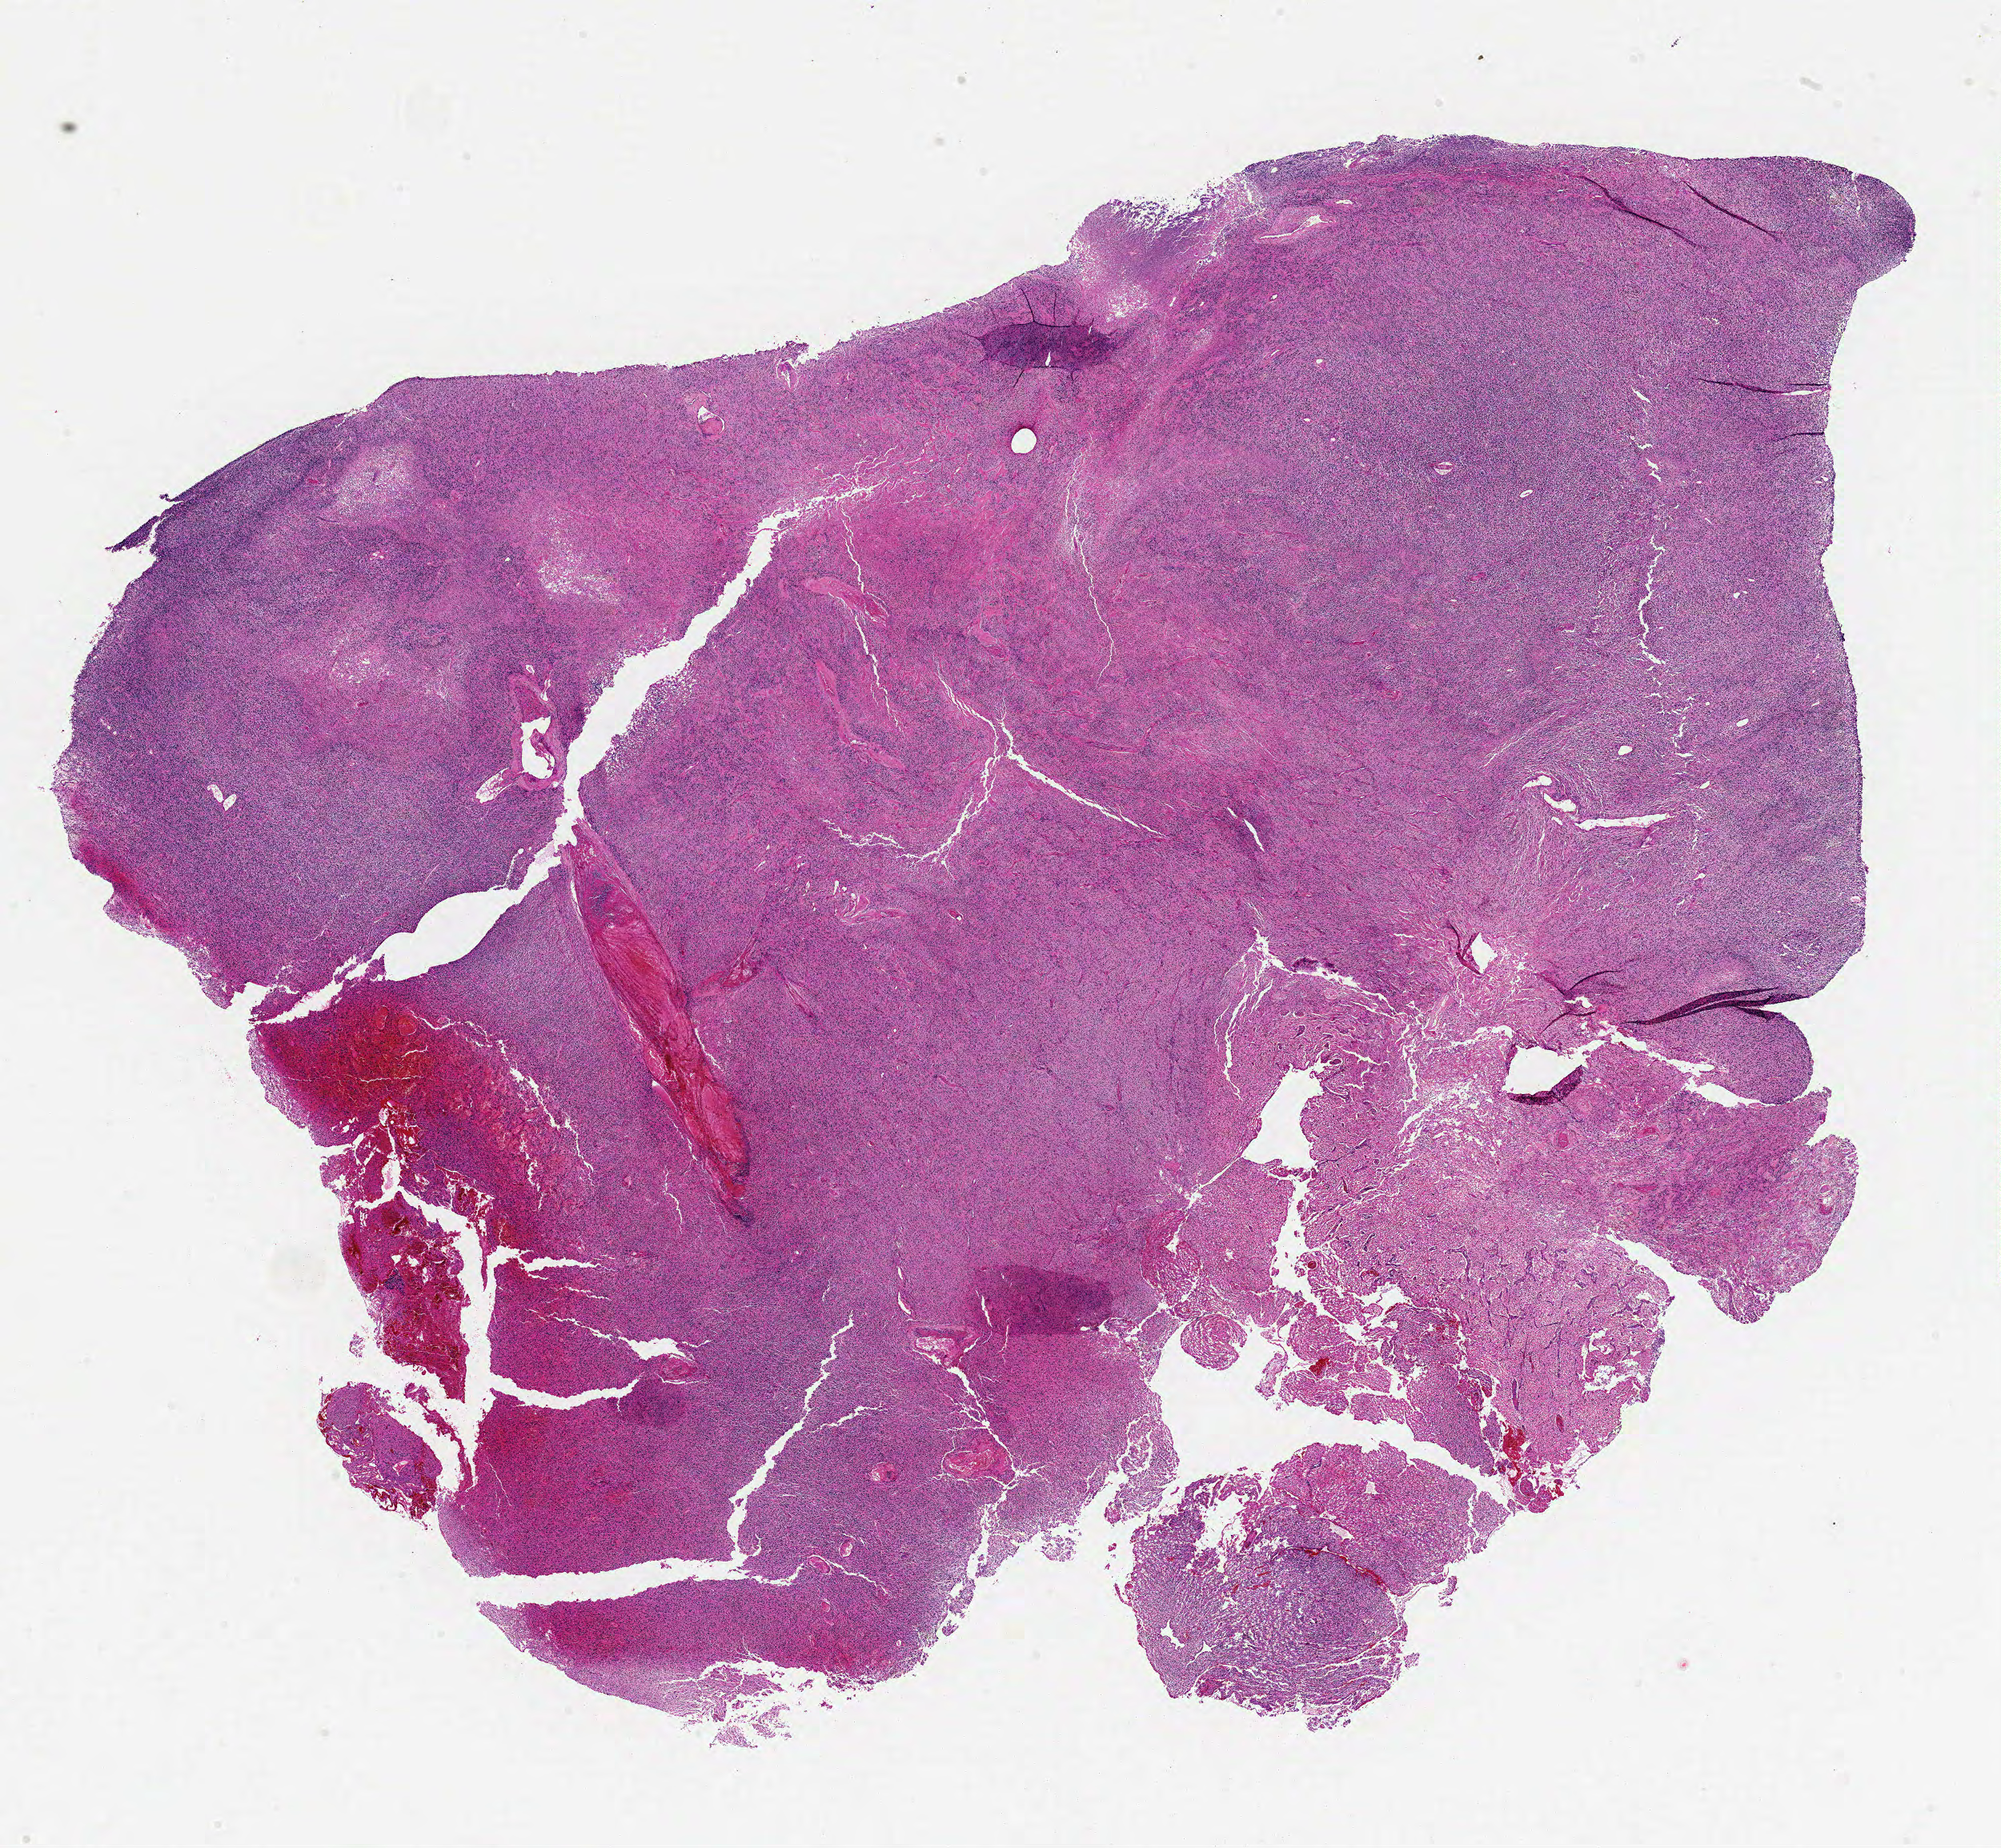
Digitized Hematoxylin and eosin (H&E) stained tissue section (whole slide) — a low-resolution overview of the entire scanned area, about 20.0 x 18.5 mm; formalin-fixed paraffin-embedded (FFPE) diagnostic section; sample: primary tumour, brain. Female, age 61 years at initial diagnosis.
- histologic diagnosis: Glioblastoma